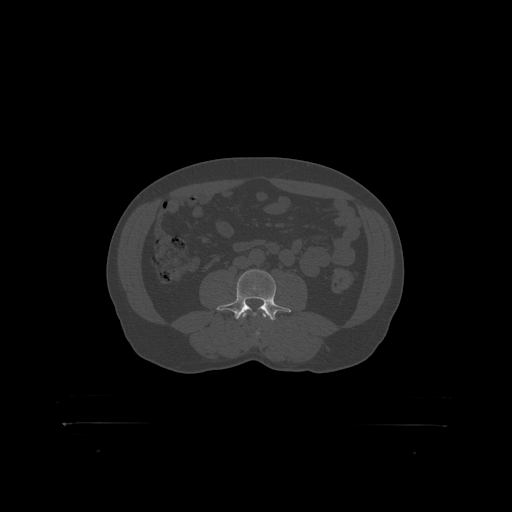
CT including the spine, one axial slice. Bone window (W 1800 / L 400 HU). 1.25 mm slice thickness. 512 × 512 image matrix, field of view 650 × 650 mm. Patient: male, 46 years. From the clinical record (not read from this slice): primary cancer: skin.
Annotated regions visible in this slice (semi-automatically segmented with operator editing):
- L3 vertebra: box from (x=242, y=313) to (x=267, y=318) px
- L4 vertebra: (x=220, y=270)–(x=289, y=317)